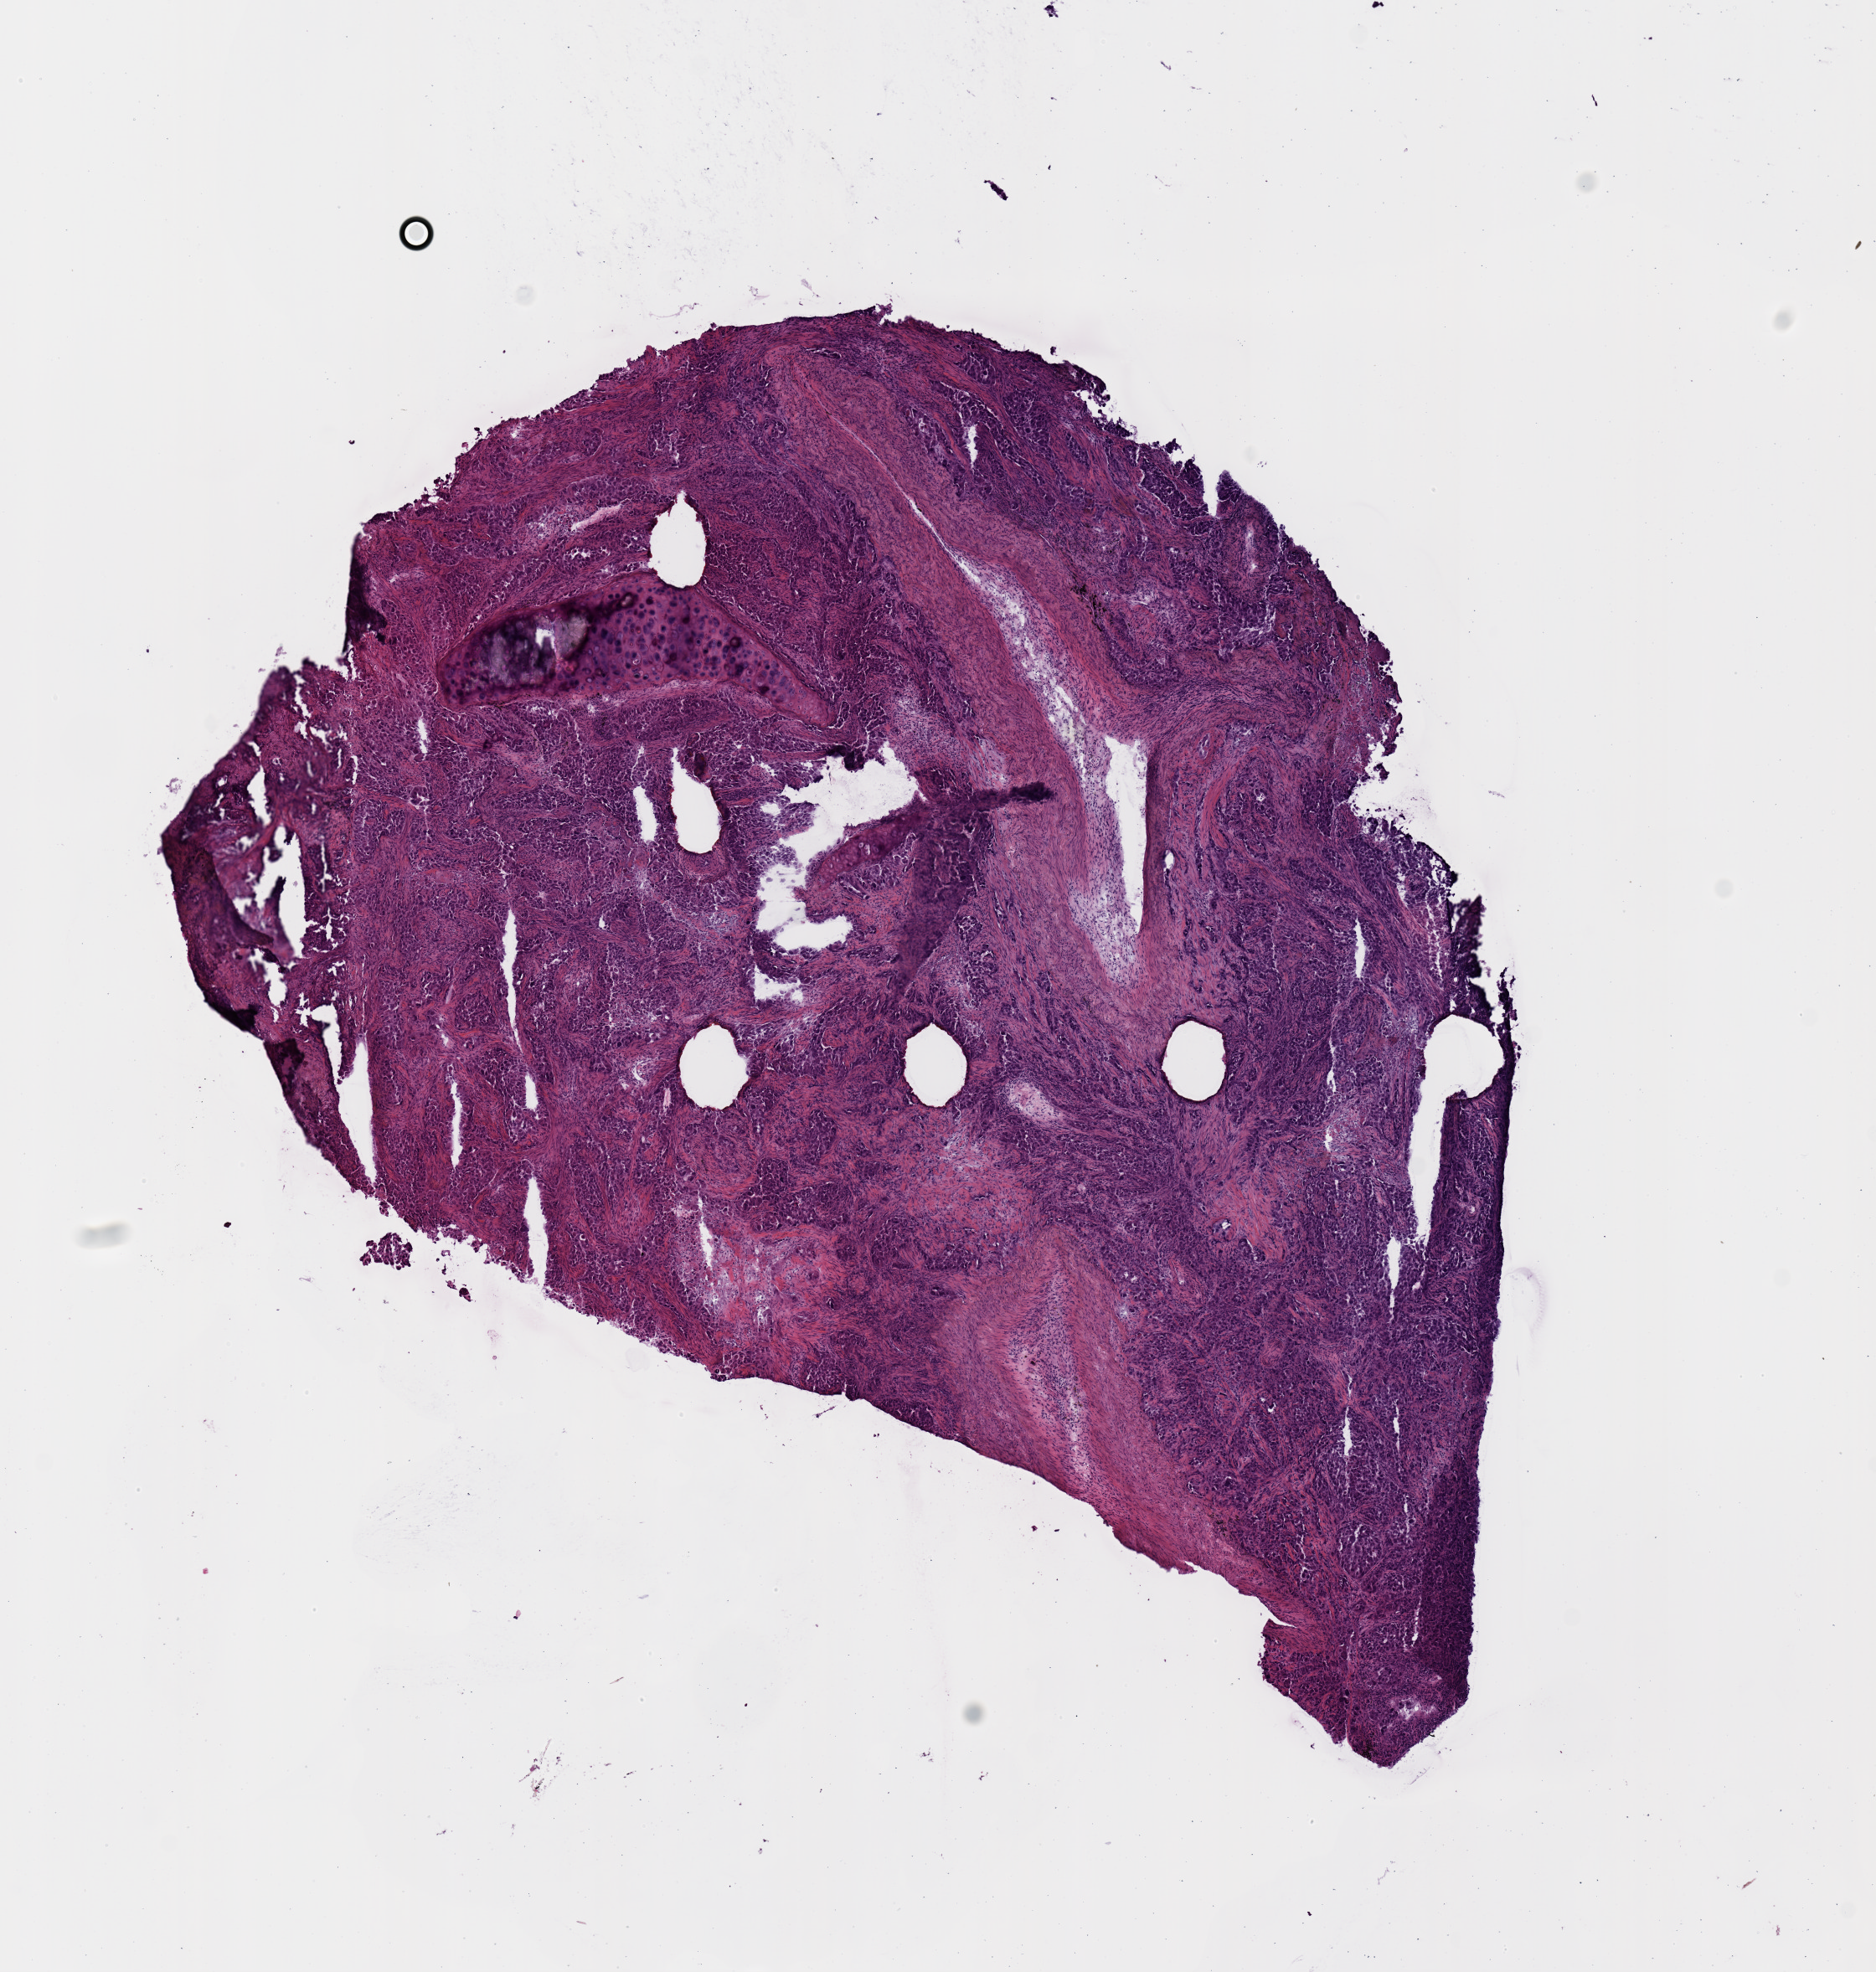
Hematoxylin and eosin (H&E) stained whole-slide image — a low-resolution overview of the entire scanned area, about 8.9 x 9.3 mm; frozen section from the top of the tissue portion; lung, primary tumour sample. Female patient; age at initial diagnosis 71 years. Composition of this section per pathologist review: tumour cells 100%, tumour nuclei 65%, normal cells 0%, stromal cells 0%, necrosis 0%. Inflammatory infiltration, as recorded: lymphocyte infiltration 10%, monocyte infiltration 2%, neutrophil infiltration 10%.
Histologic diagnosis: Acinar cell carcinoma (upper lobe, lung). AJCC pathologic stage: IB.